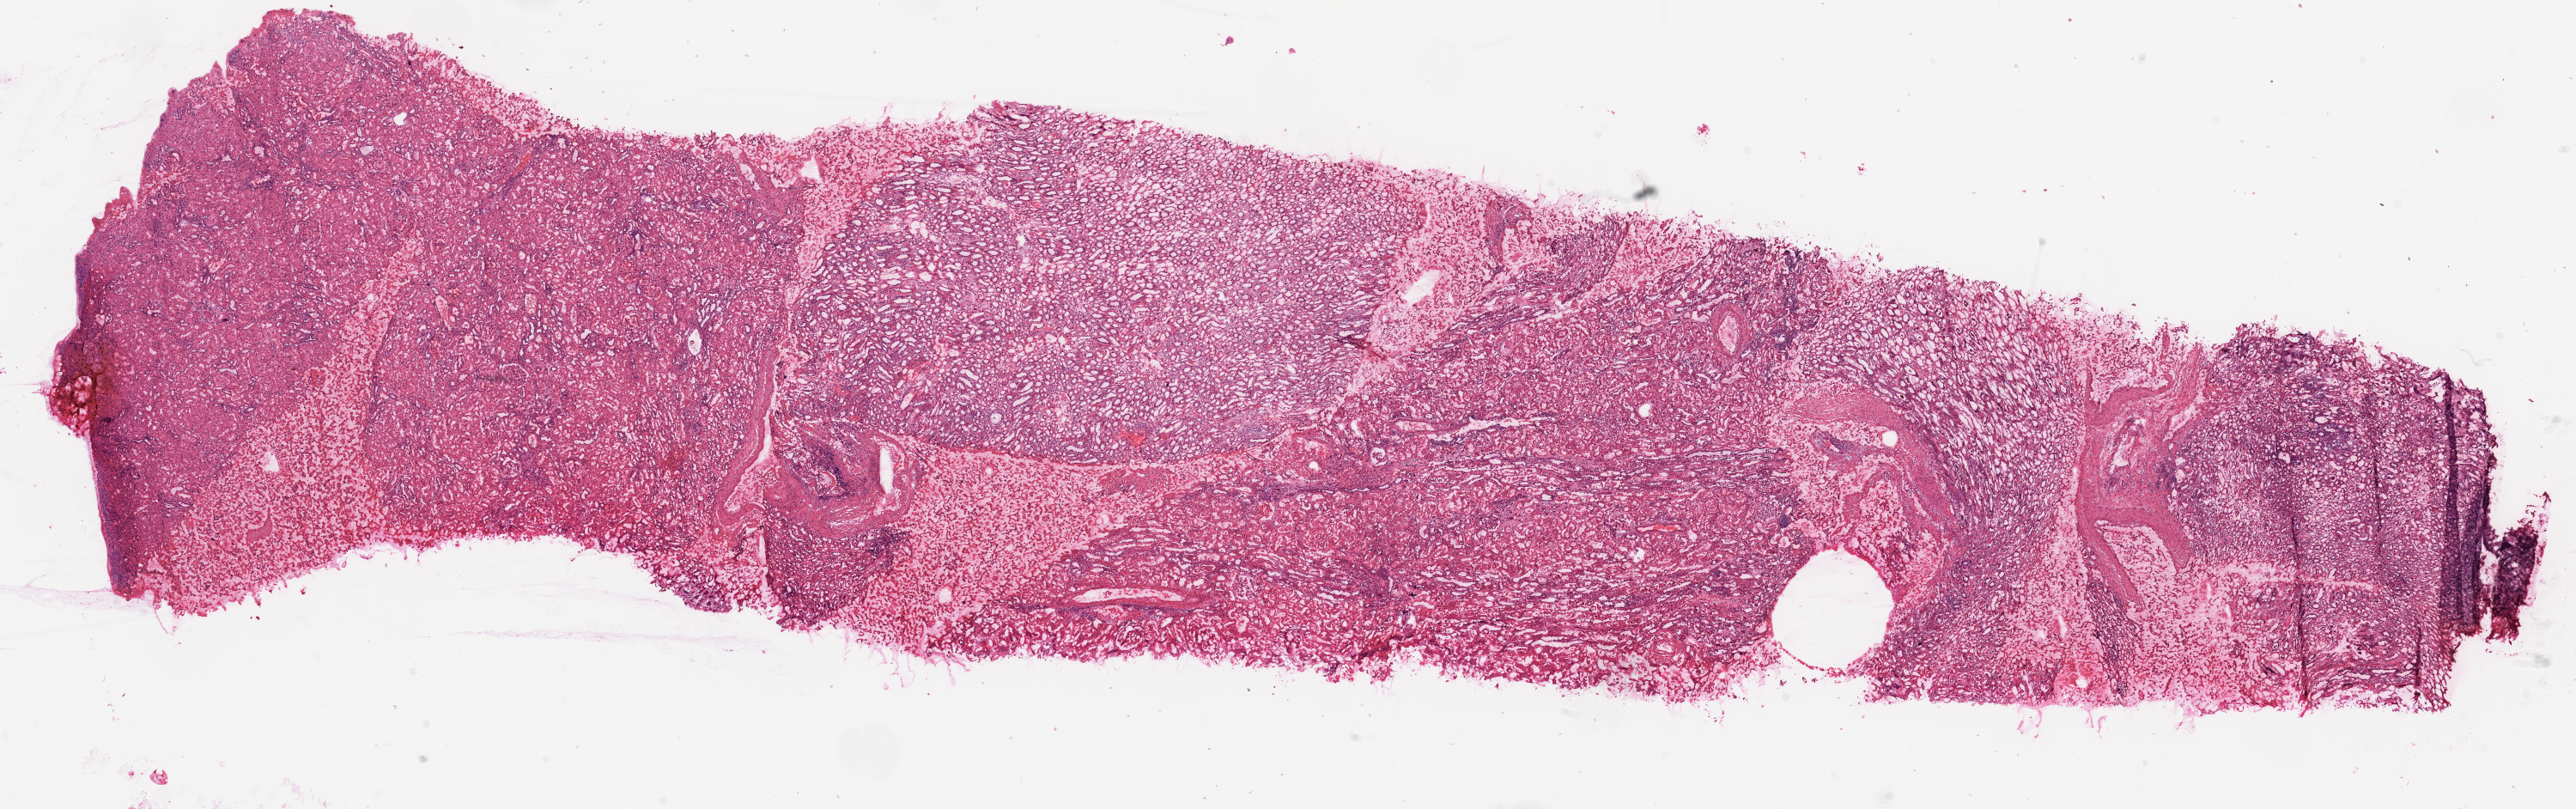
Whole-slide histology image, Hematoxylin and eosin (H&E) stained — a low-resolution overview of the entire scanned area, about 24.1 x 7.6 mm (slide scanned at 20x); frozen section; solid tissue normal (non-tumour tissue) sample from the kidney. Male patient; age at initial diagnosis 42 years.
- this section: solid tissue normal (non-tumour) sample from the same patient
- patient diagnosis: Clear cell adenocarcinoma, NOS